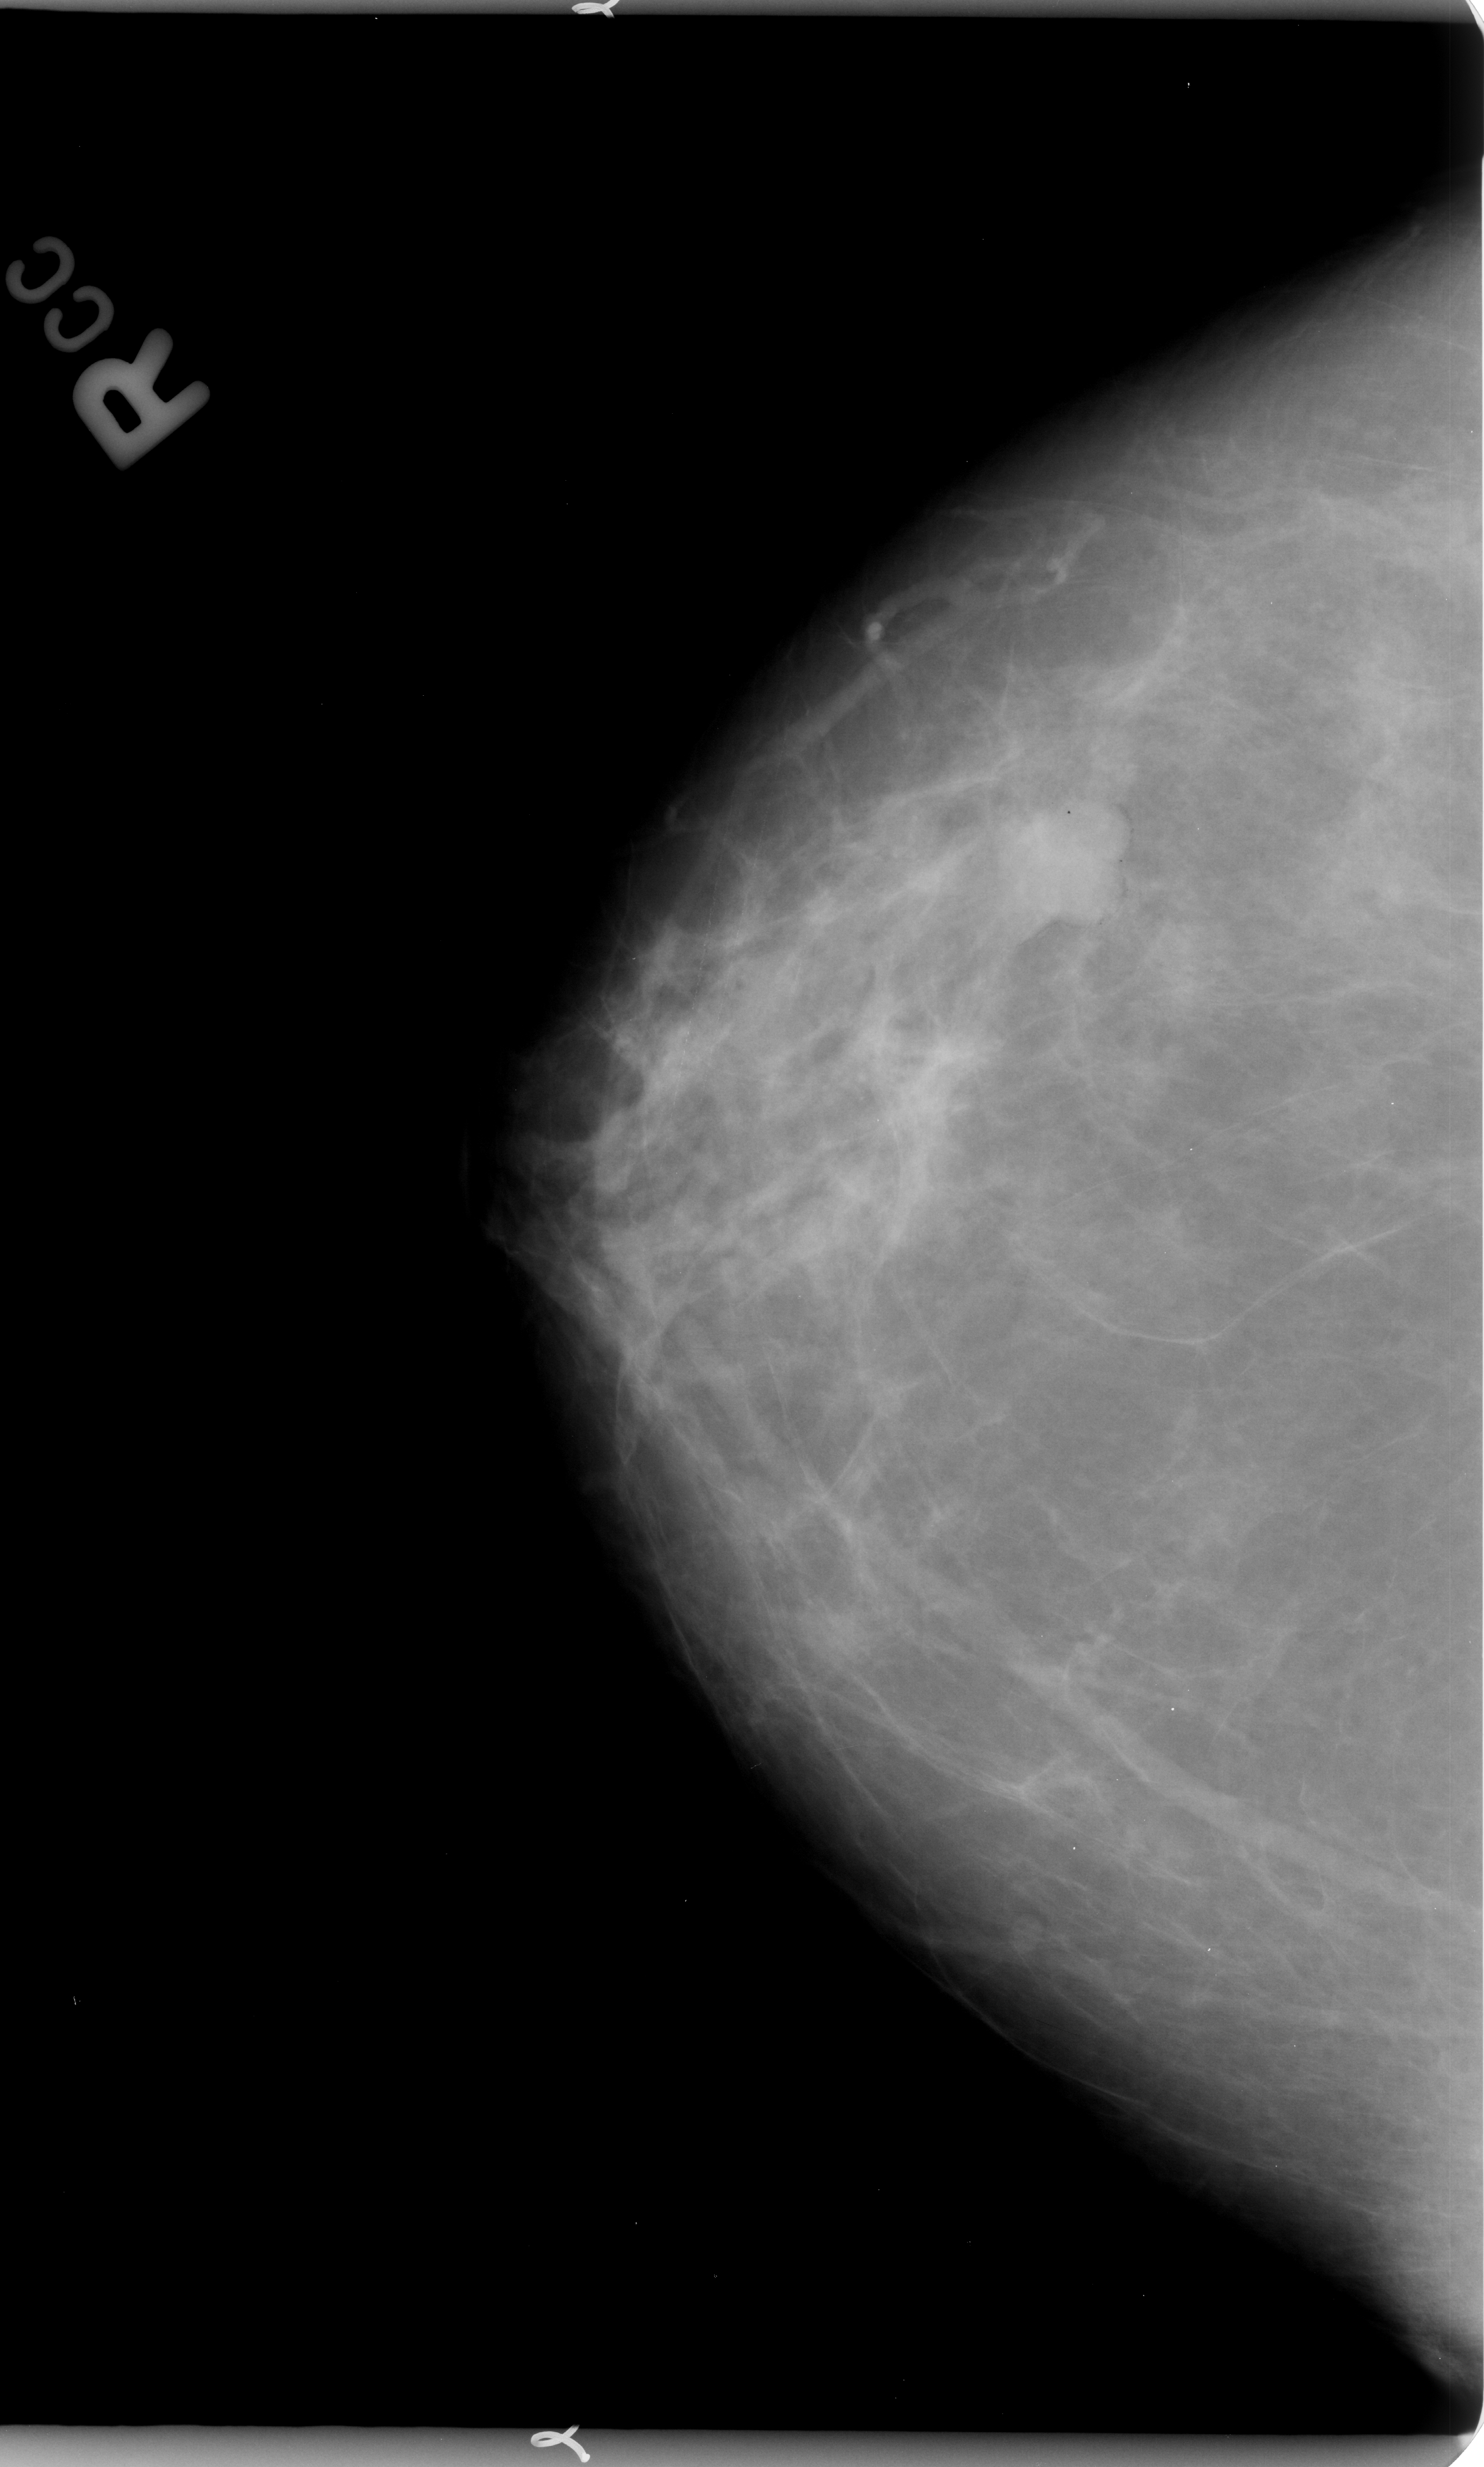
Digitized screen-film mammogram; right breast; craniocaudal (CC) view; breast composition: scattered fibroglandular densities (BI-RADS density category 2 of 4).
Radiologist-marked abnormalities on this image: mass, shape lobulated, margins circumscribed / ill defined; BI-RADS assessment category 4; subtlety rating 4 on a 1 (subtle) to 5 (obvious) scale; pathology result (as recorded, not read from the image): malignant.